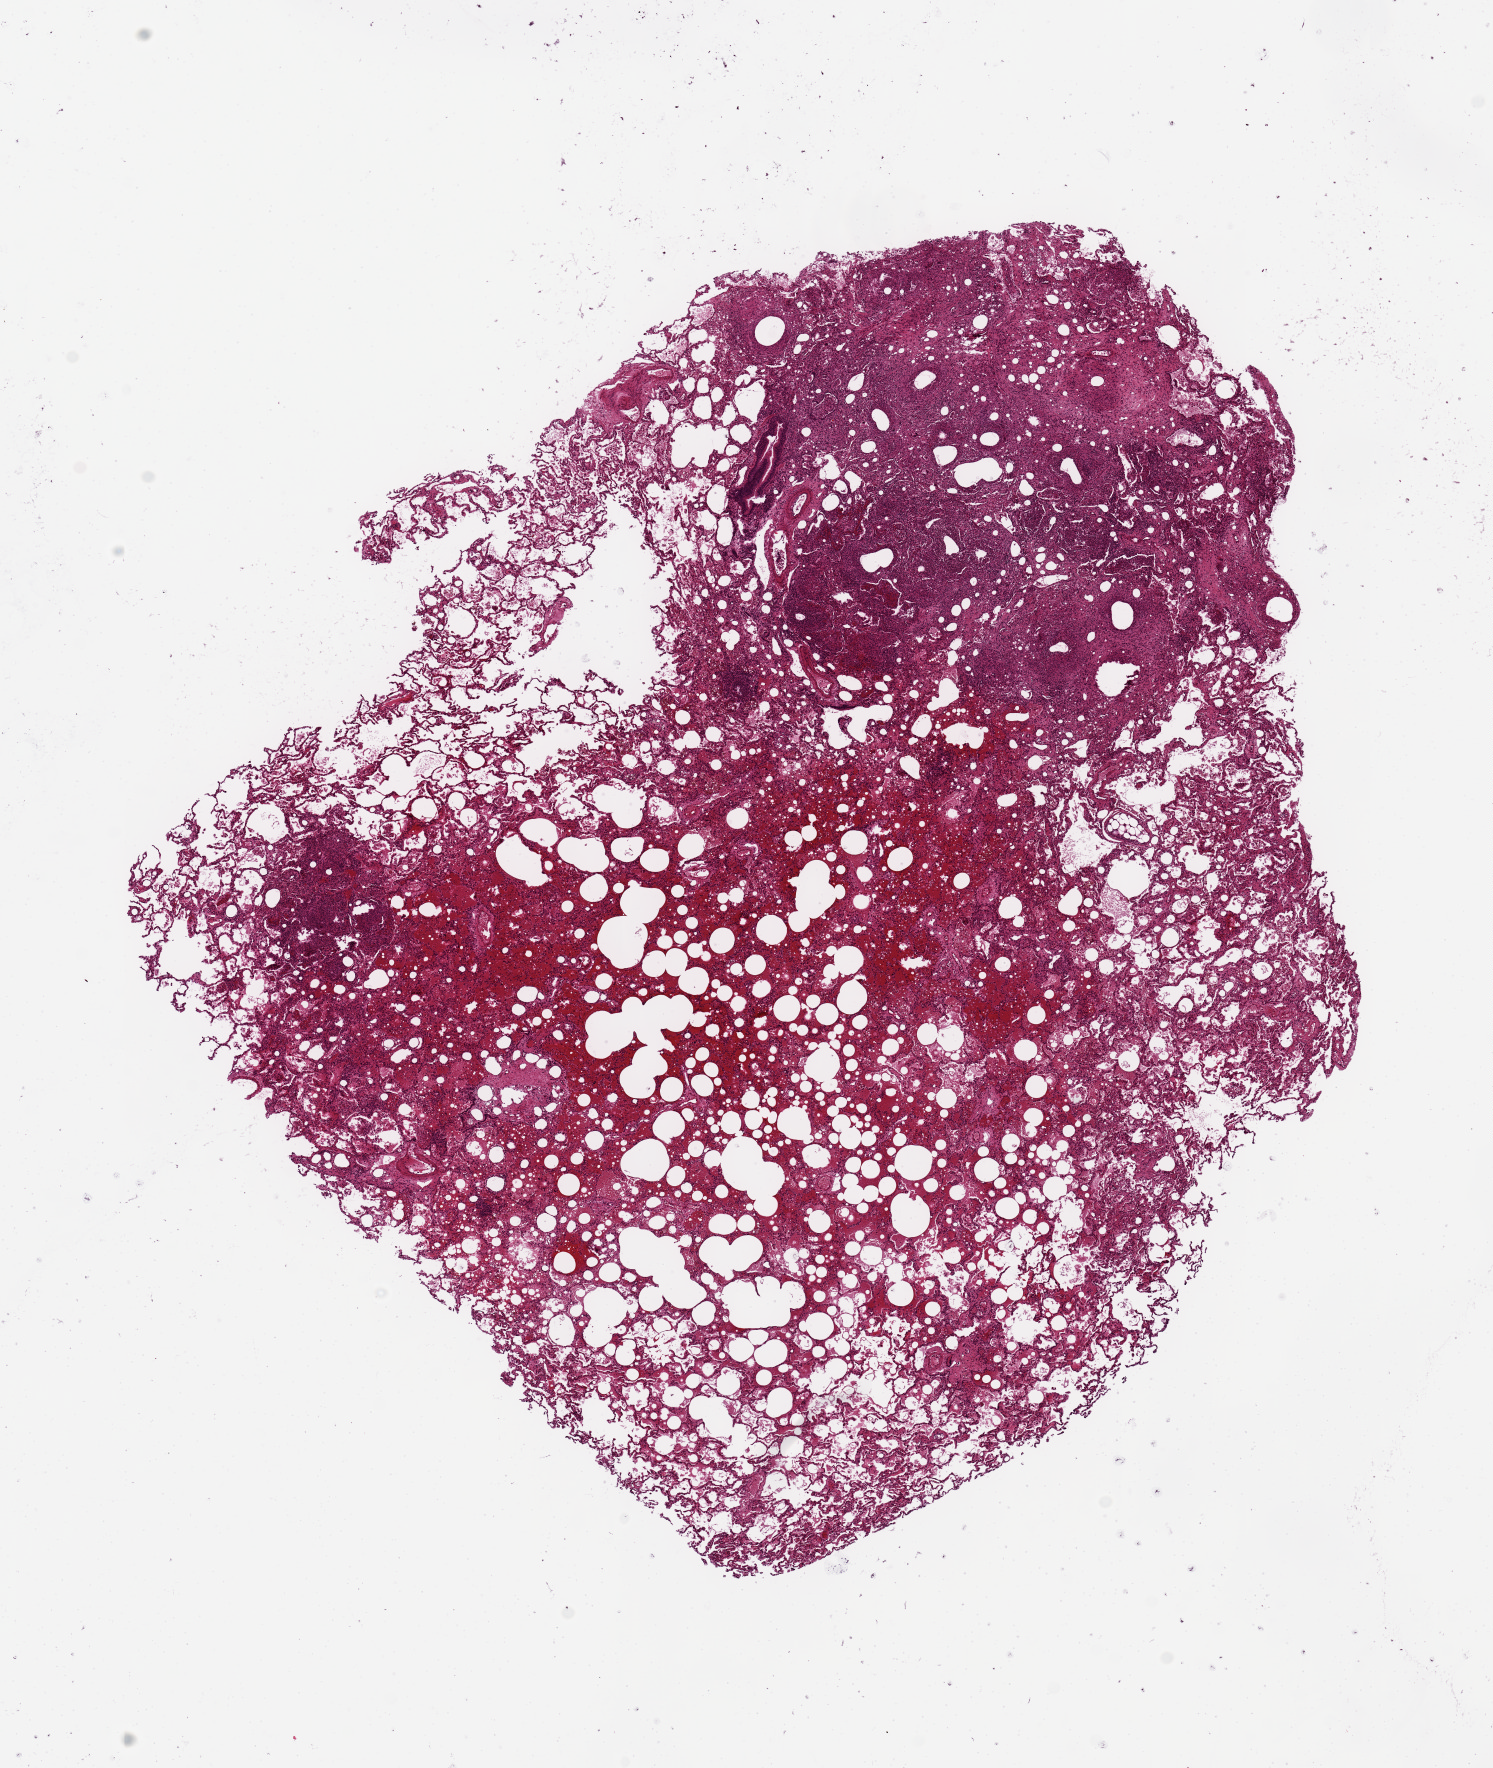
Digitized haematoxylin and eosin-stained section, low-resolution overview of the scanned area, about 11.8 x 14.0 mm. PAXgene-fixed, paraffin-embedded tissue. Section of lung (target tissue). Donor tissue sample. Female donor.
Pathologist's review note for this sample: ~9x8mm. Dense areas granulomatous pneumonitis /hemorrhage. Foreign body giant cells, and lipoid-like structures. Probable Aspiration pneumonia.